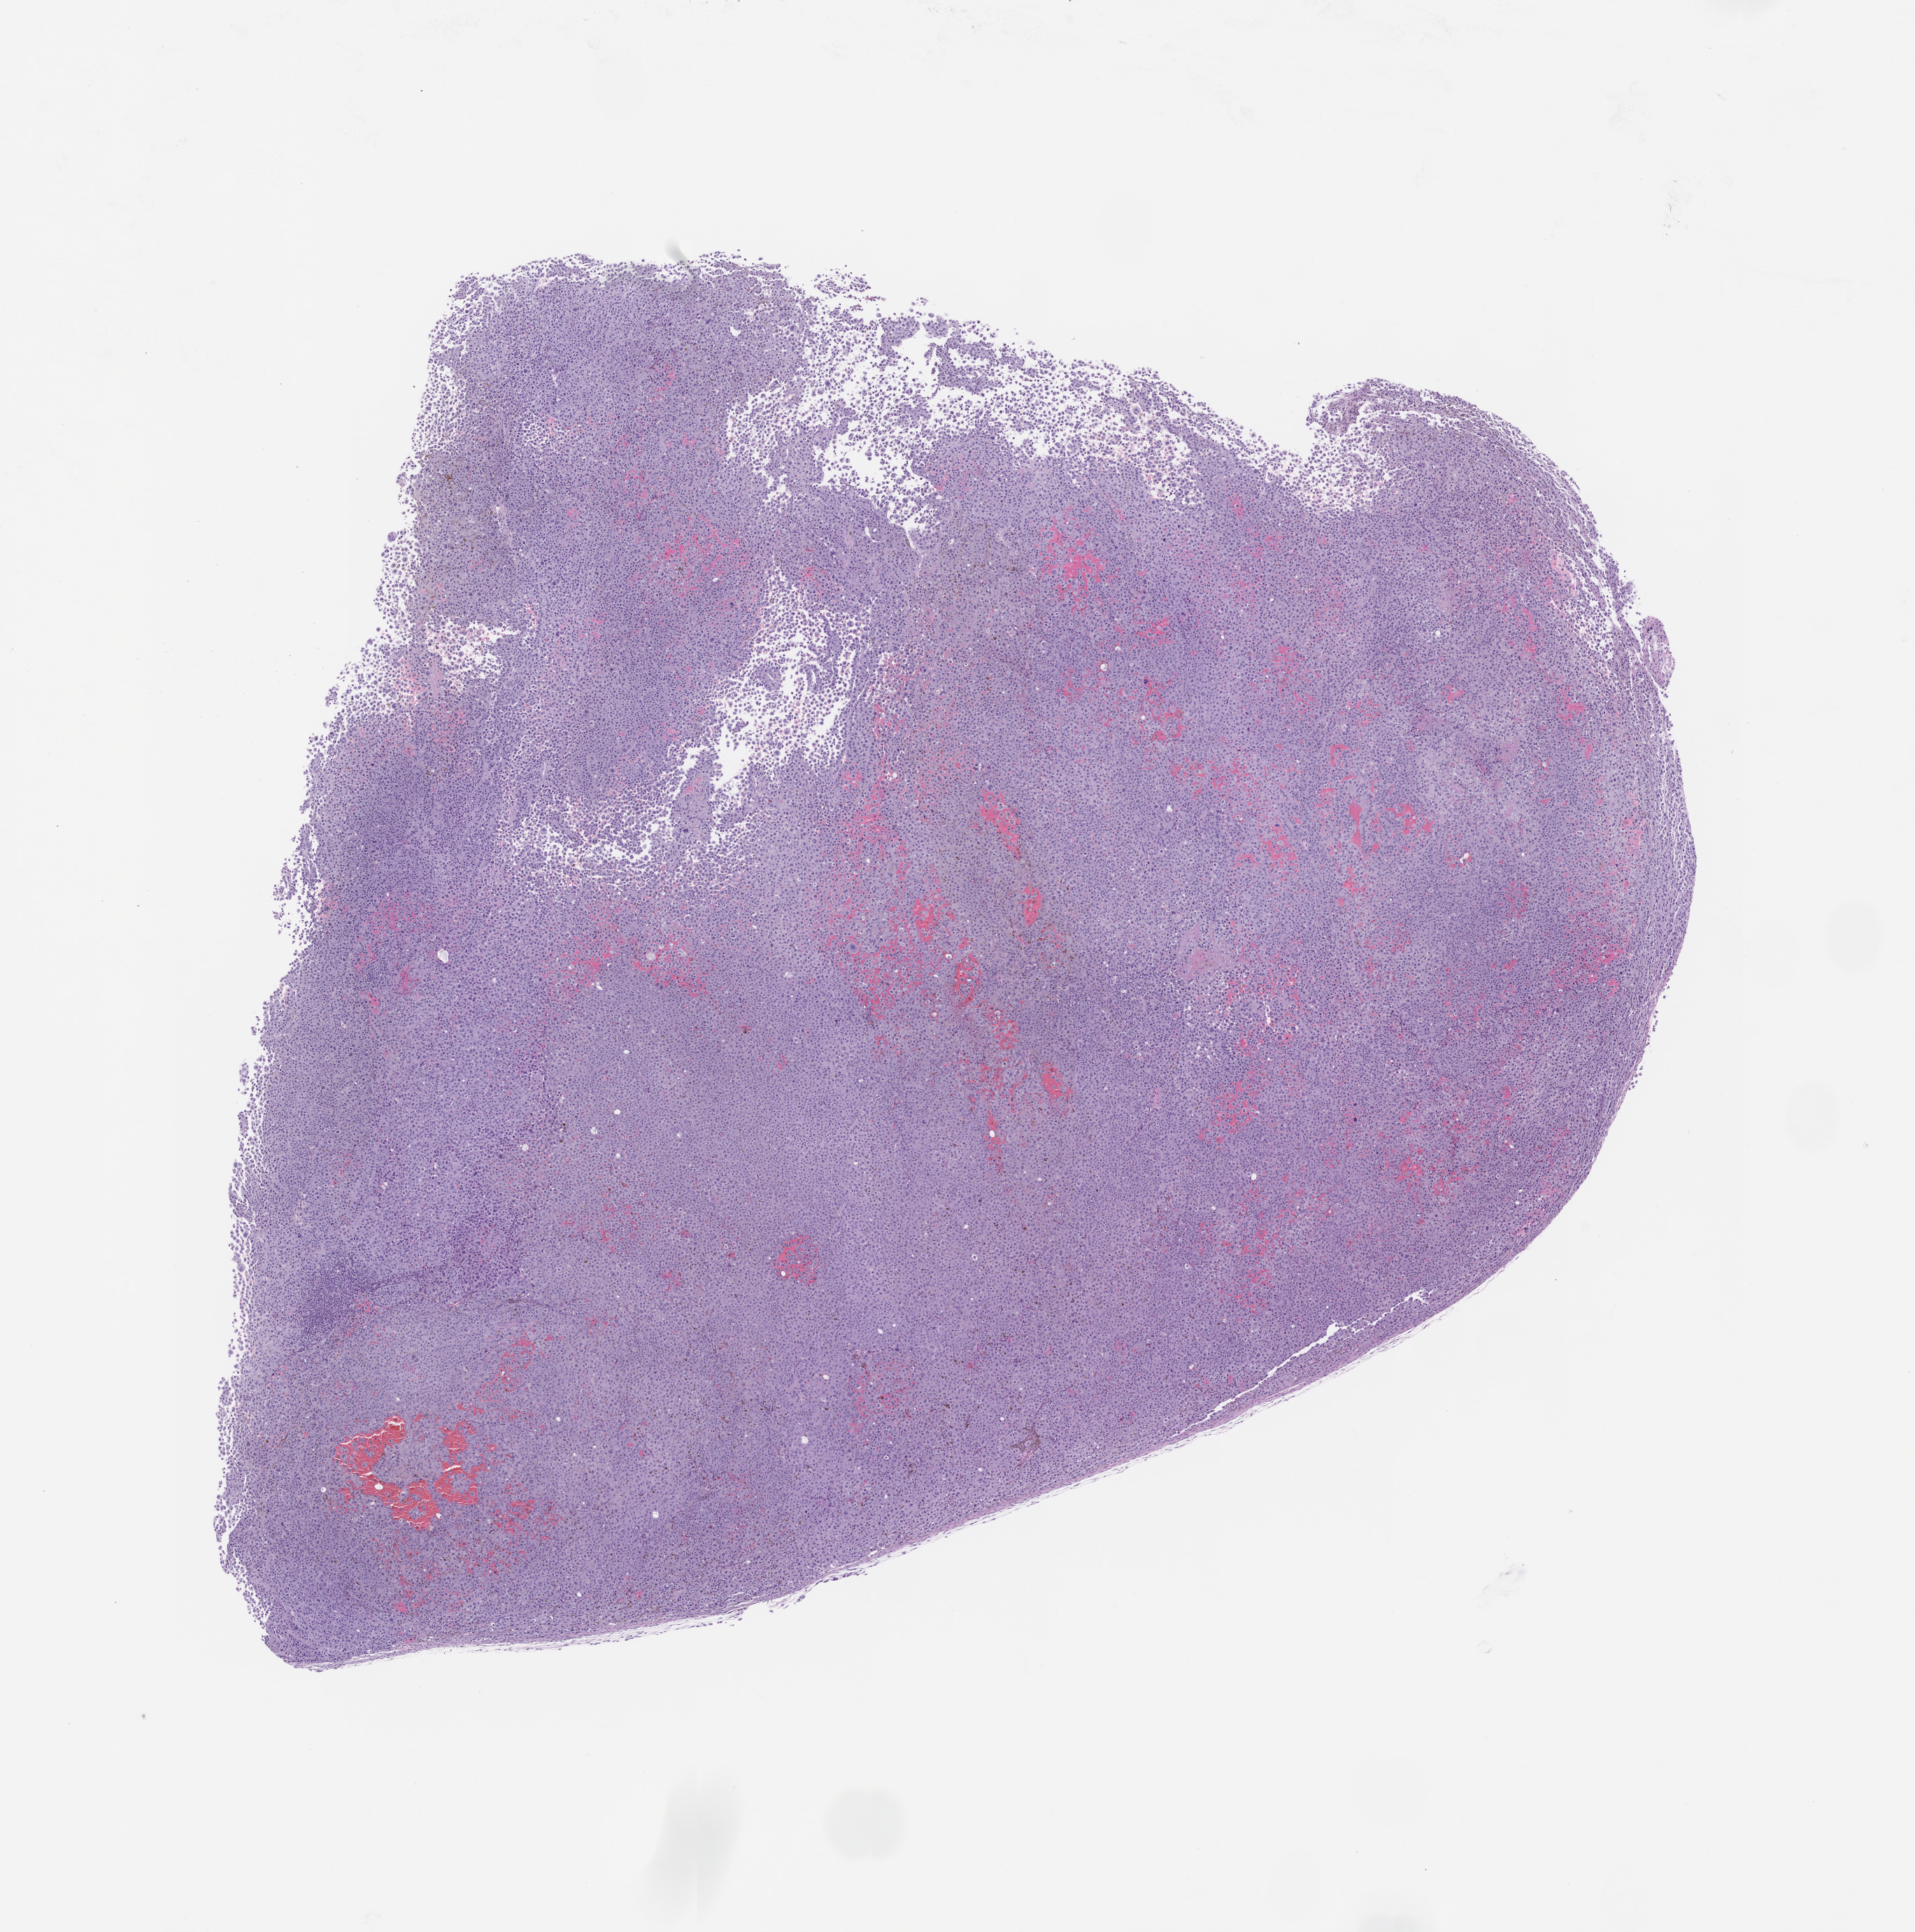
Haematoxylin and eosin whole-slide image of a patient-derived xenograft (PDX) tumor grown in a mouse, passage 1 — shown as a low-resolution overview of the whole scanned area (about 11.0 x 11.1 mm), formalin-fixed paraffin-embedded section, tumor site category: skin.
Originating patient diagnosis: Melanoma.